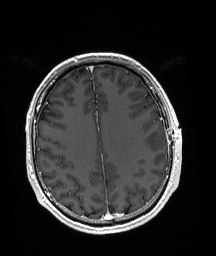
Brain MRI from a brain-tumour surgery series, one axial slice; position 67 of 192 along the scan axis; T1-weighted post-contrast; 1 mm slice thickness; 216 × 256 image matrix, field of view 211 × 250 mm. Case-level facts recorded for this patient, not image findings: histopathology: Astrocytoma; WHO grade: 3; IDH mutation: yes.
Structures marked on this image (manually delineated by an expert):
- tumour: bounding box (x1, y1, x2, y2) in pixels: (143, 130, 165, 152)